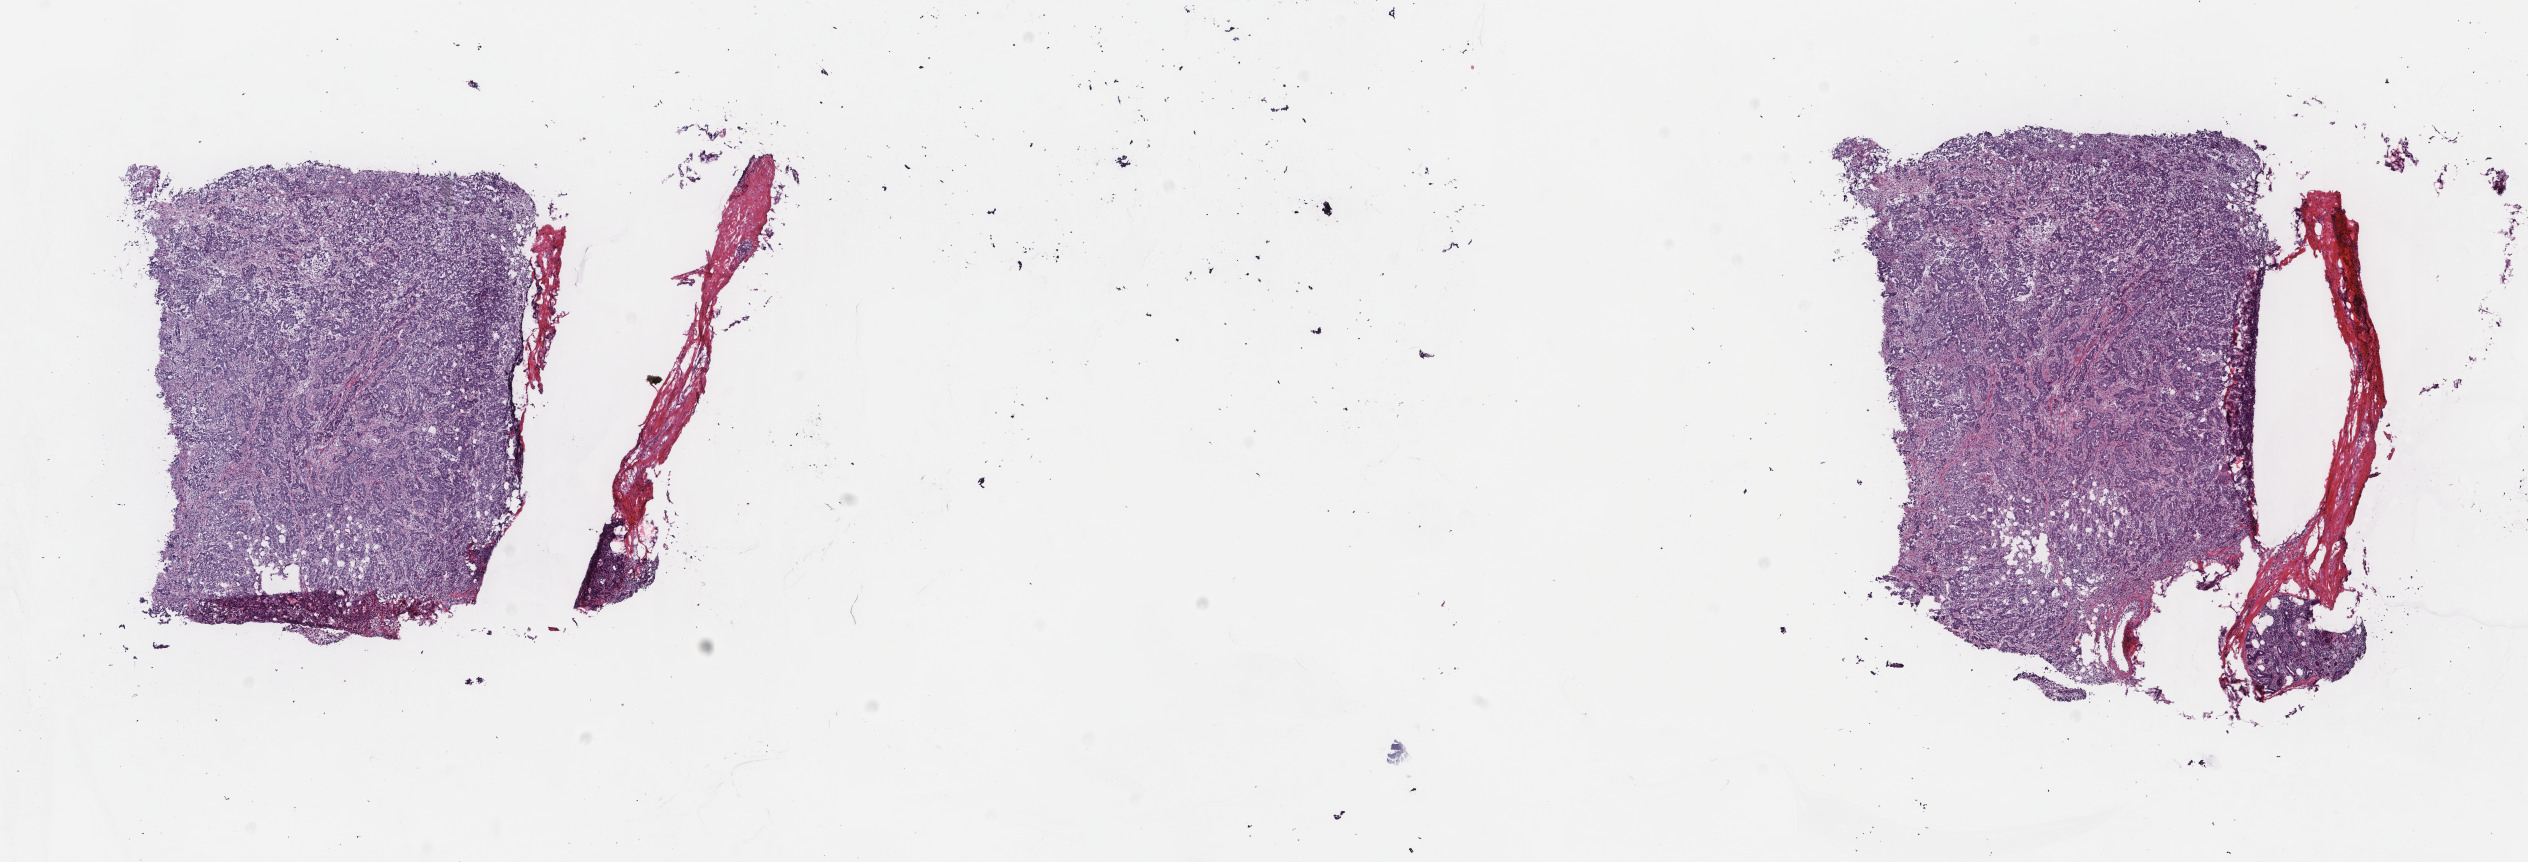
Whole-slide histology image, Hematoxylin and eosin (H&E) stained, a low-resolution overview of the entire scanned area, about 20.1 x 6.8 mm (acquisition: 40x scan), frozen section, breast, primary tumour sample. Female, age 50 years at initial diagnosis. Composition of this section per pathologist review: tumour cells 95%, tumour nuclei 70%, normal cells 0%, stromal cells 5%, necrosis 0%. Inflammatory infiltration, as recorded: lymphocyte infiltration 0%, monocyte infiltration 0%, neutrophil infiltration 0%.
AJCC pathologic stage: IIIA (6th edition). Laterality: left. Lymph nodes positive (case pathology): 9 of 30 examined. Pathologic diagnosis: Infiltrating duct carcinoma, NOS.